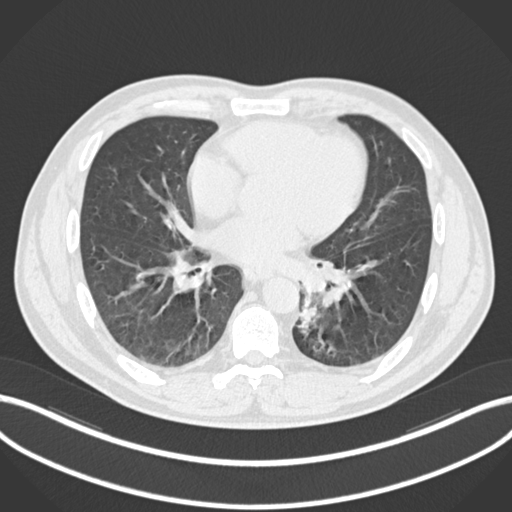
Chest CT, one axial slice. Position 97 of 223 along the scan axis. 120 kVp. Lung window (W 1500 / L -600 HU). 1 mm slice thickness. 512 × 512 image matrix. Male patient, age 50 years. Case-level facts recorded for this patient, not image findings: clinical TNM (as recorded): T2a N3 M0.
Outlined on this slice (rectangle marked by the reading radiologist):
- lung tumour (recorded histology: squamous cell carcinoma): bounding box <292,292,320,336> (left, top, right, bottom; pixels)